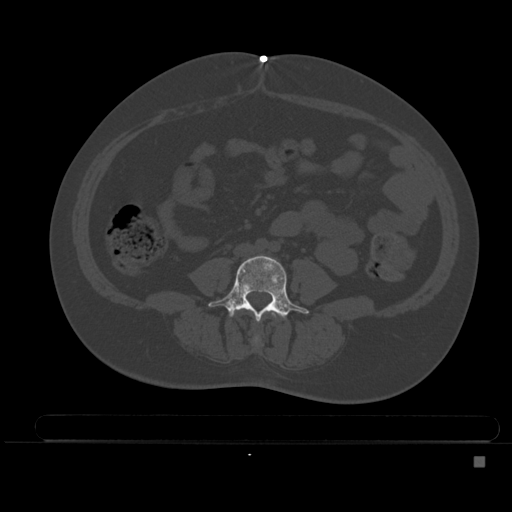
CT including the spine, one axial slice. Position 133 of 495 along the scan axis. Bone window (W 1800 / L 400 HU). 1.5 mm slice thickness. 512 × 512 image matrix, field of view 404 × 404 mm. Female patient, age 33 years. From the clinical record (not read from this slice): primary cancer: breast; vertebrae with lytic lesions (as recorded): T1.
Outlined on this slice (semi-automatic segmentation, software-assisted and operator-edited):
- L3 vertebra: box from (x=252, y=310) to (x=278, y=344) px
- L4 vertebra: (x=208, y=255)–(x=309, y=322)